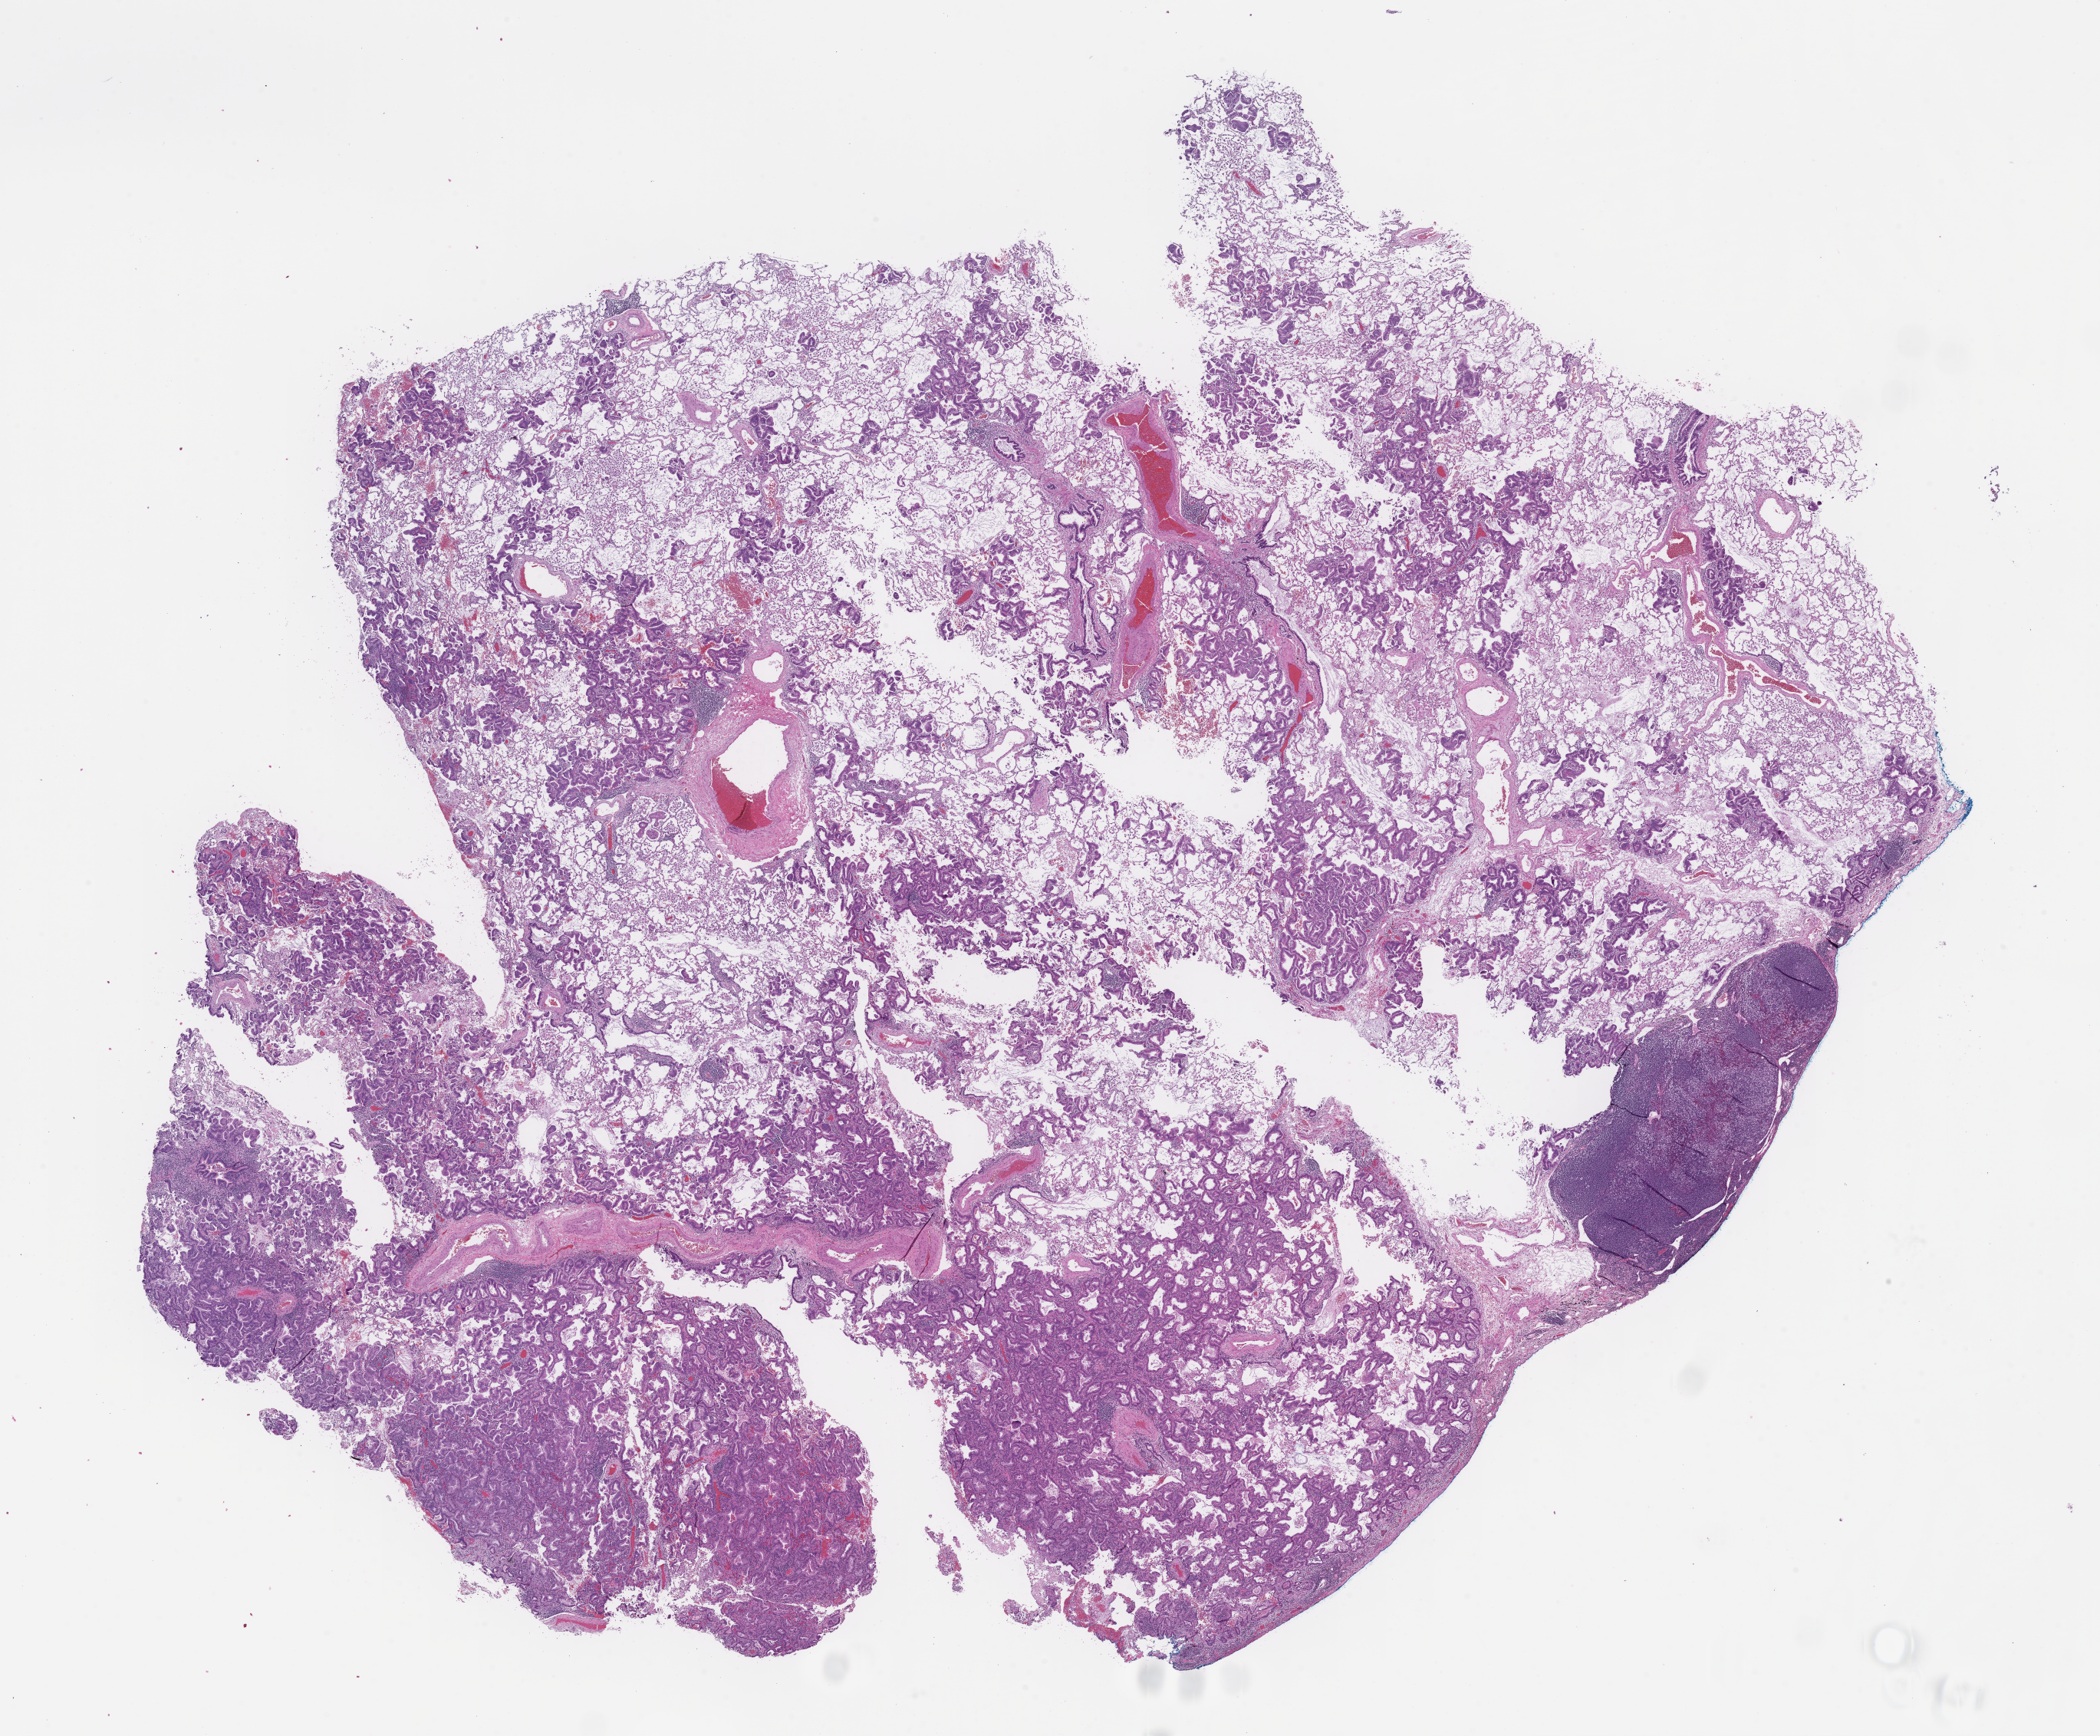
Hematoxylin and eosin (H&E) whole-slide image, whole scanned area (about 22.1 x 18.3 mm) shown as a low-resolution overview. FFPE section. Tissue site: lung. Female patient.
This section: primary tumour tissue. Diagnosis: Non-Small Cell Lung Carcinoma.